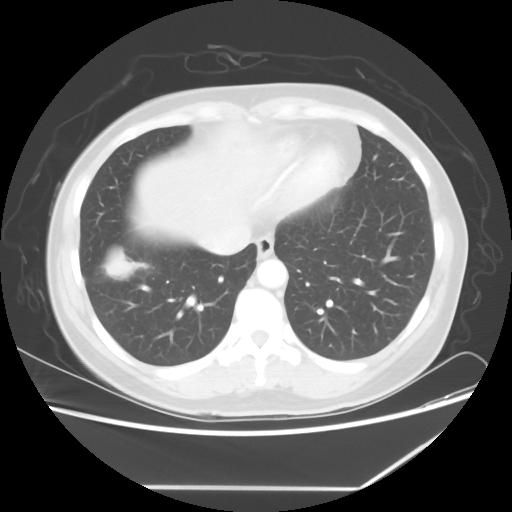
Chest CT, one axial slice; reconstruction kernel STANDARD; lung window (W 1500 / L -600 HU); 5 mm slice thickness; 512 × 512 image matrix. Female patient, age 42 years. Case-level facts recorded for this patient, not image findings: clinical TNM (as recorded): T2 N1 M0.
Annotated regions visible in this slice (rectangle marked by the reading radiologist):
- lung tumour (recorded histology: adenocarcinoma): bounding box <101,251,137,285> (left, top, right, bottom; pixels)